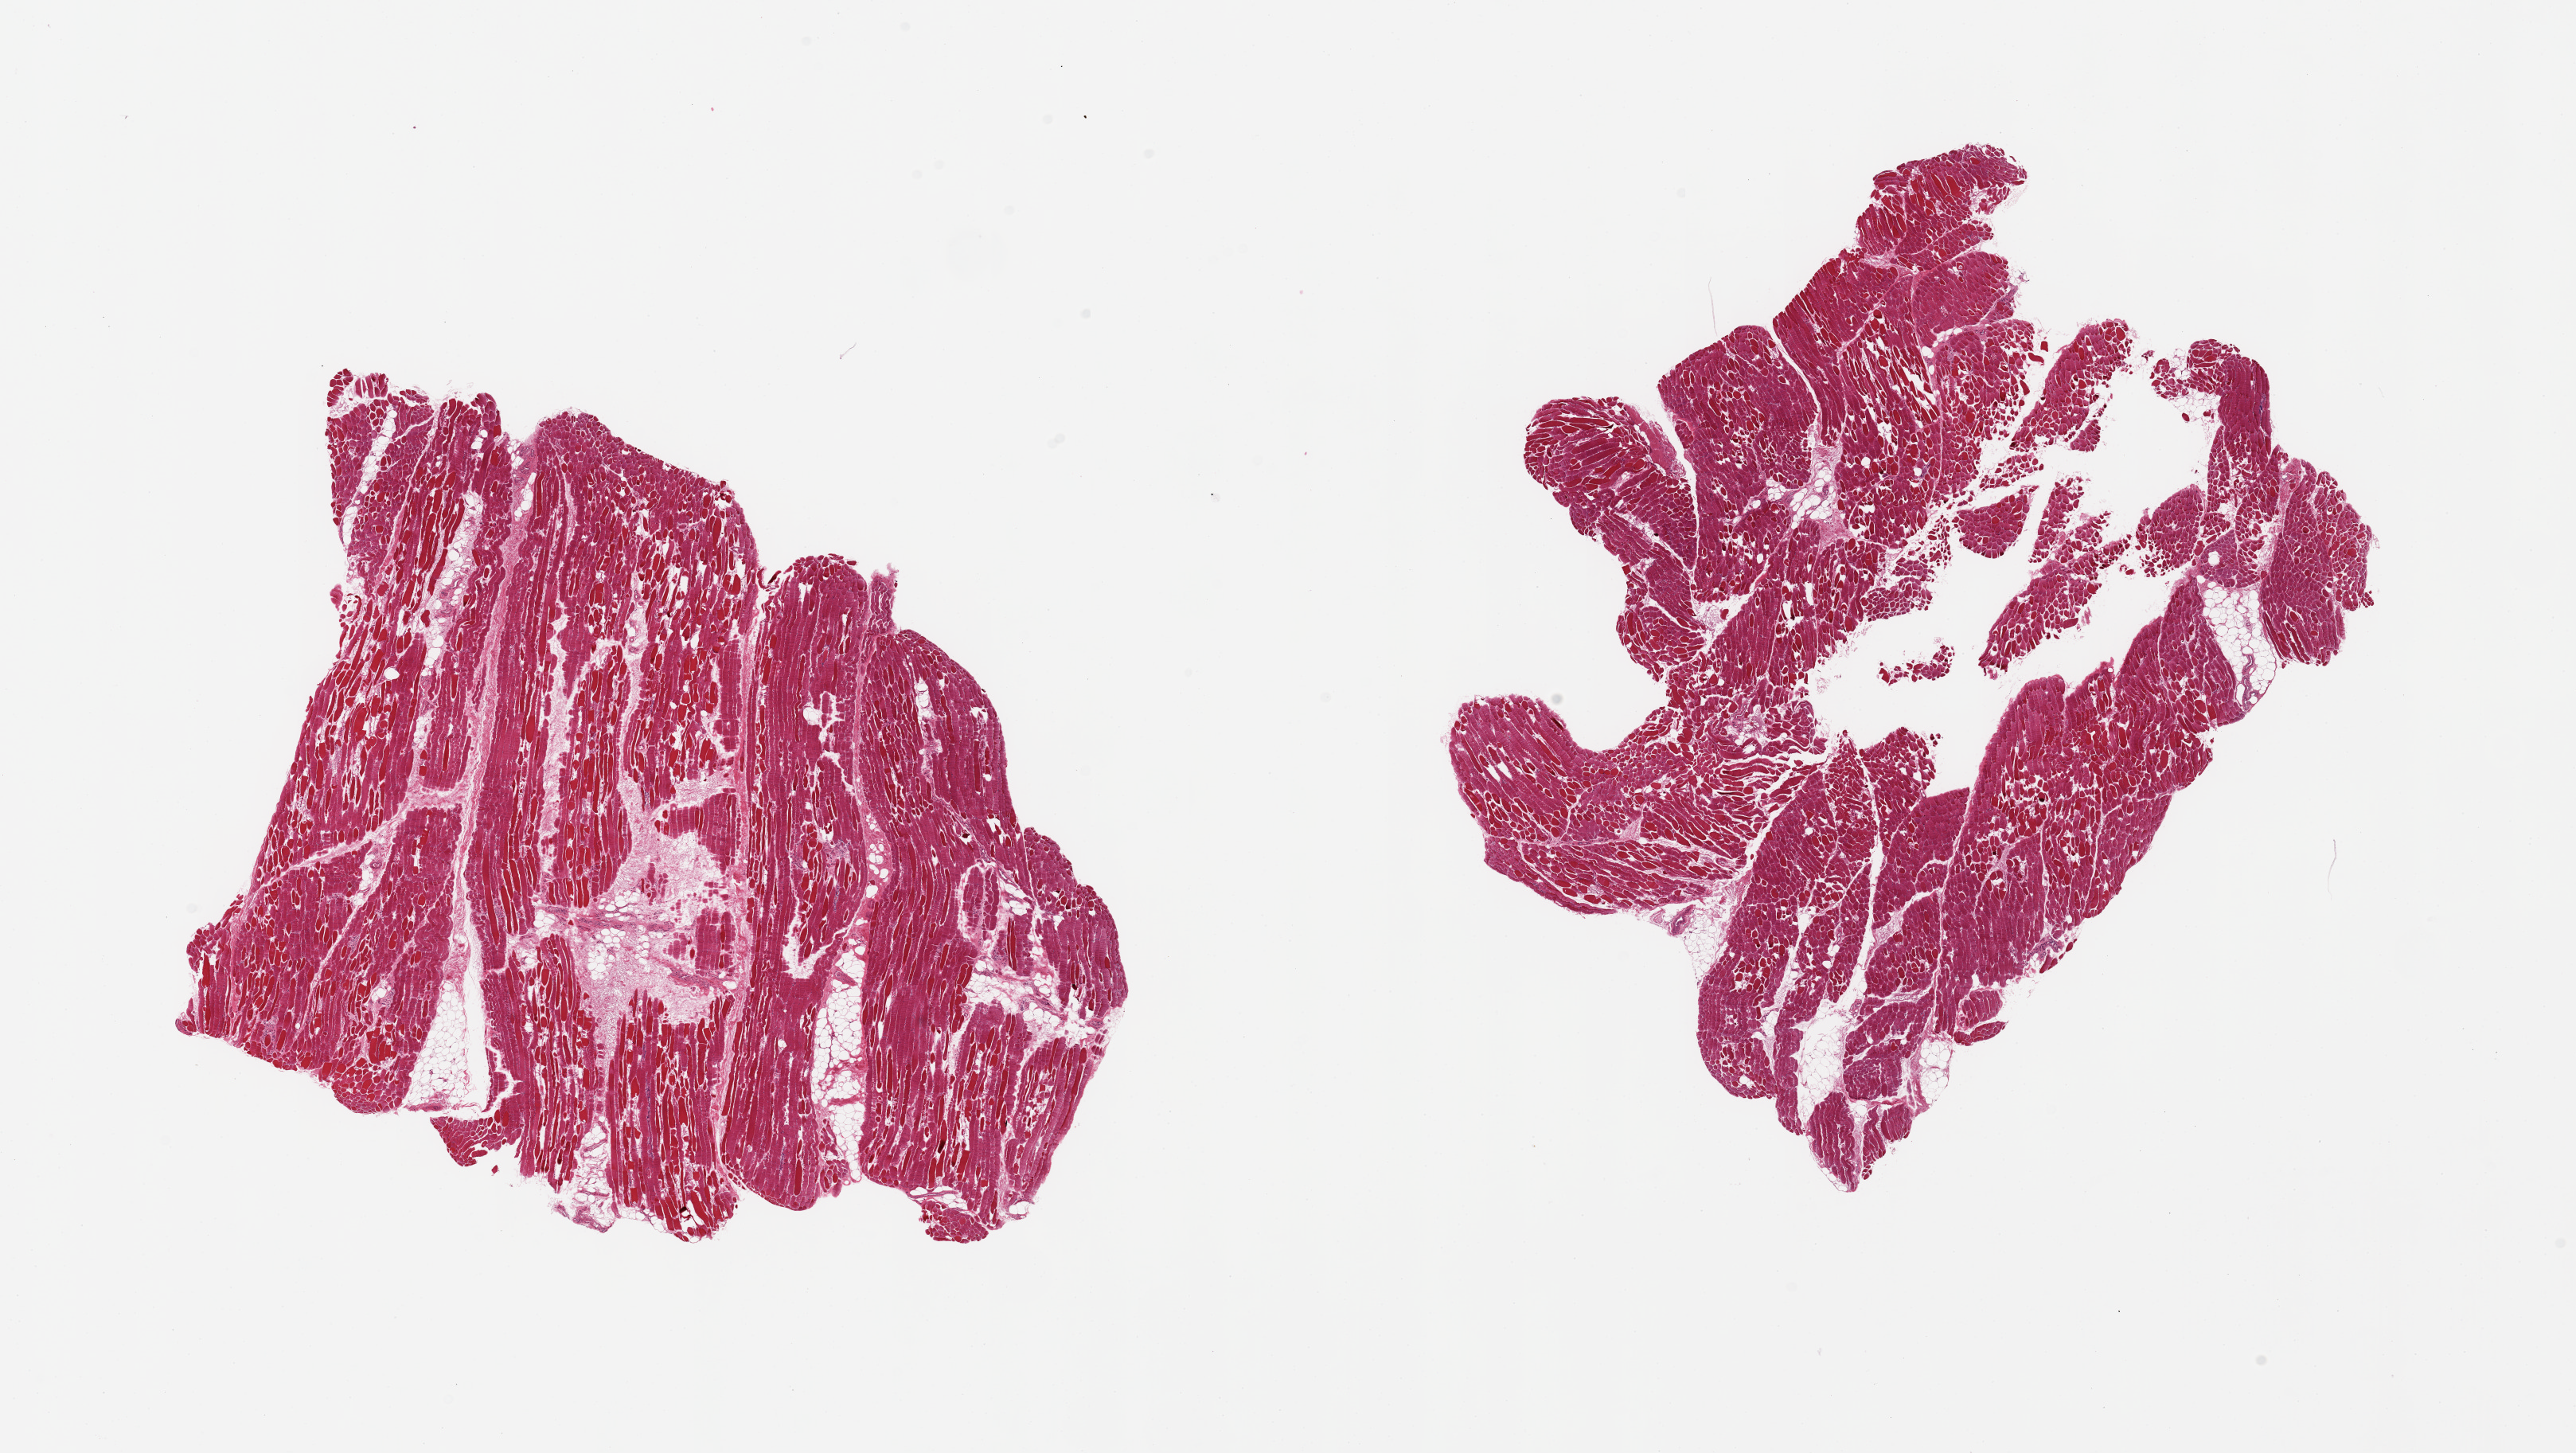
Haematoxylin and eosin whole-slide image, a low-resolution overview of the entire scanned area, about 25.6 x 14.4 mm, PAXgene-fixed, paraffin-embedded tissue, sampled site (target tissue): skeletal muscle, donor tissue sample. Donor sex: male.
Review note (as recorded): 2 pieces; ~20% of one is internal fat, second piece has large central defect (? fatty), scattered atrophic fibers.